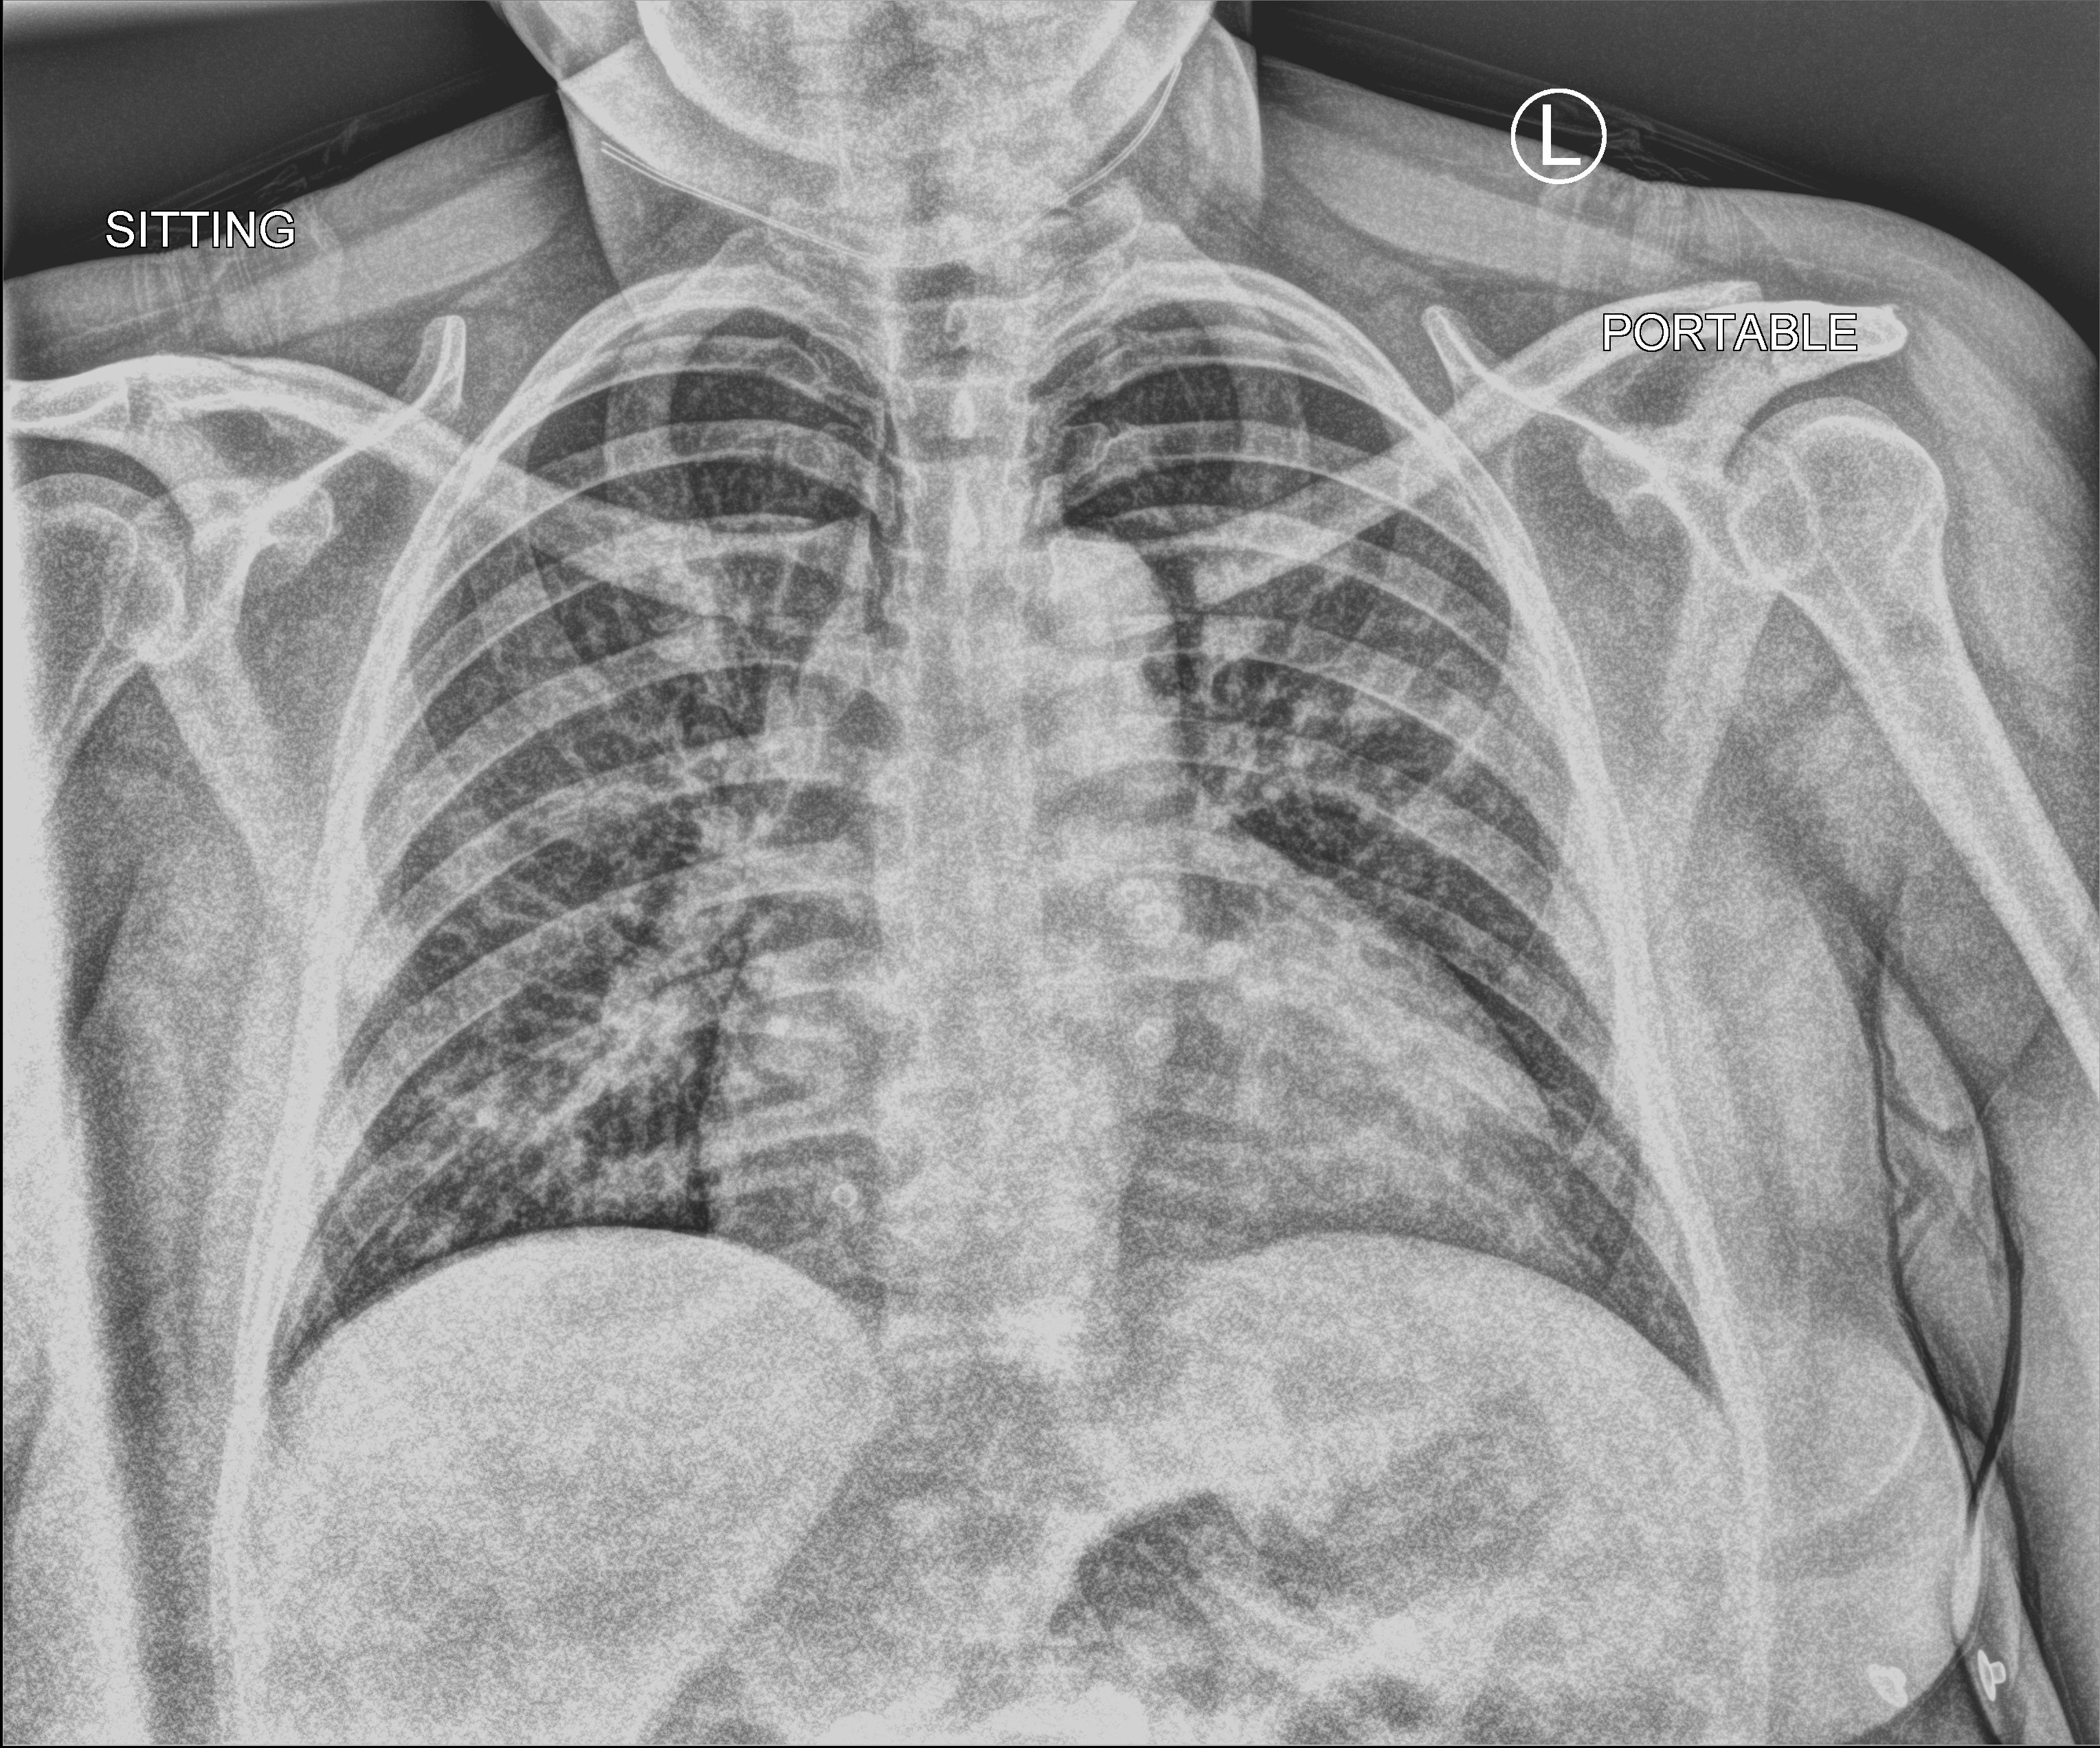
Chest X-ray (portable). Patient hospitalised with COVID-19; female, aged 18–59 years.
Hospital-stay facts (about this admission, not read from this image; timing relative to this image not recorded): mechanically ventilated during this hospital stay: no; admitted to intensive care during this hospital stay: no; length of hospital stay: 1 day.